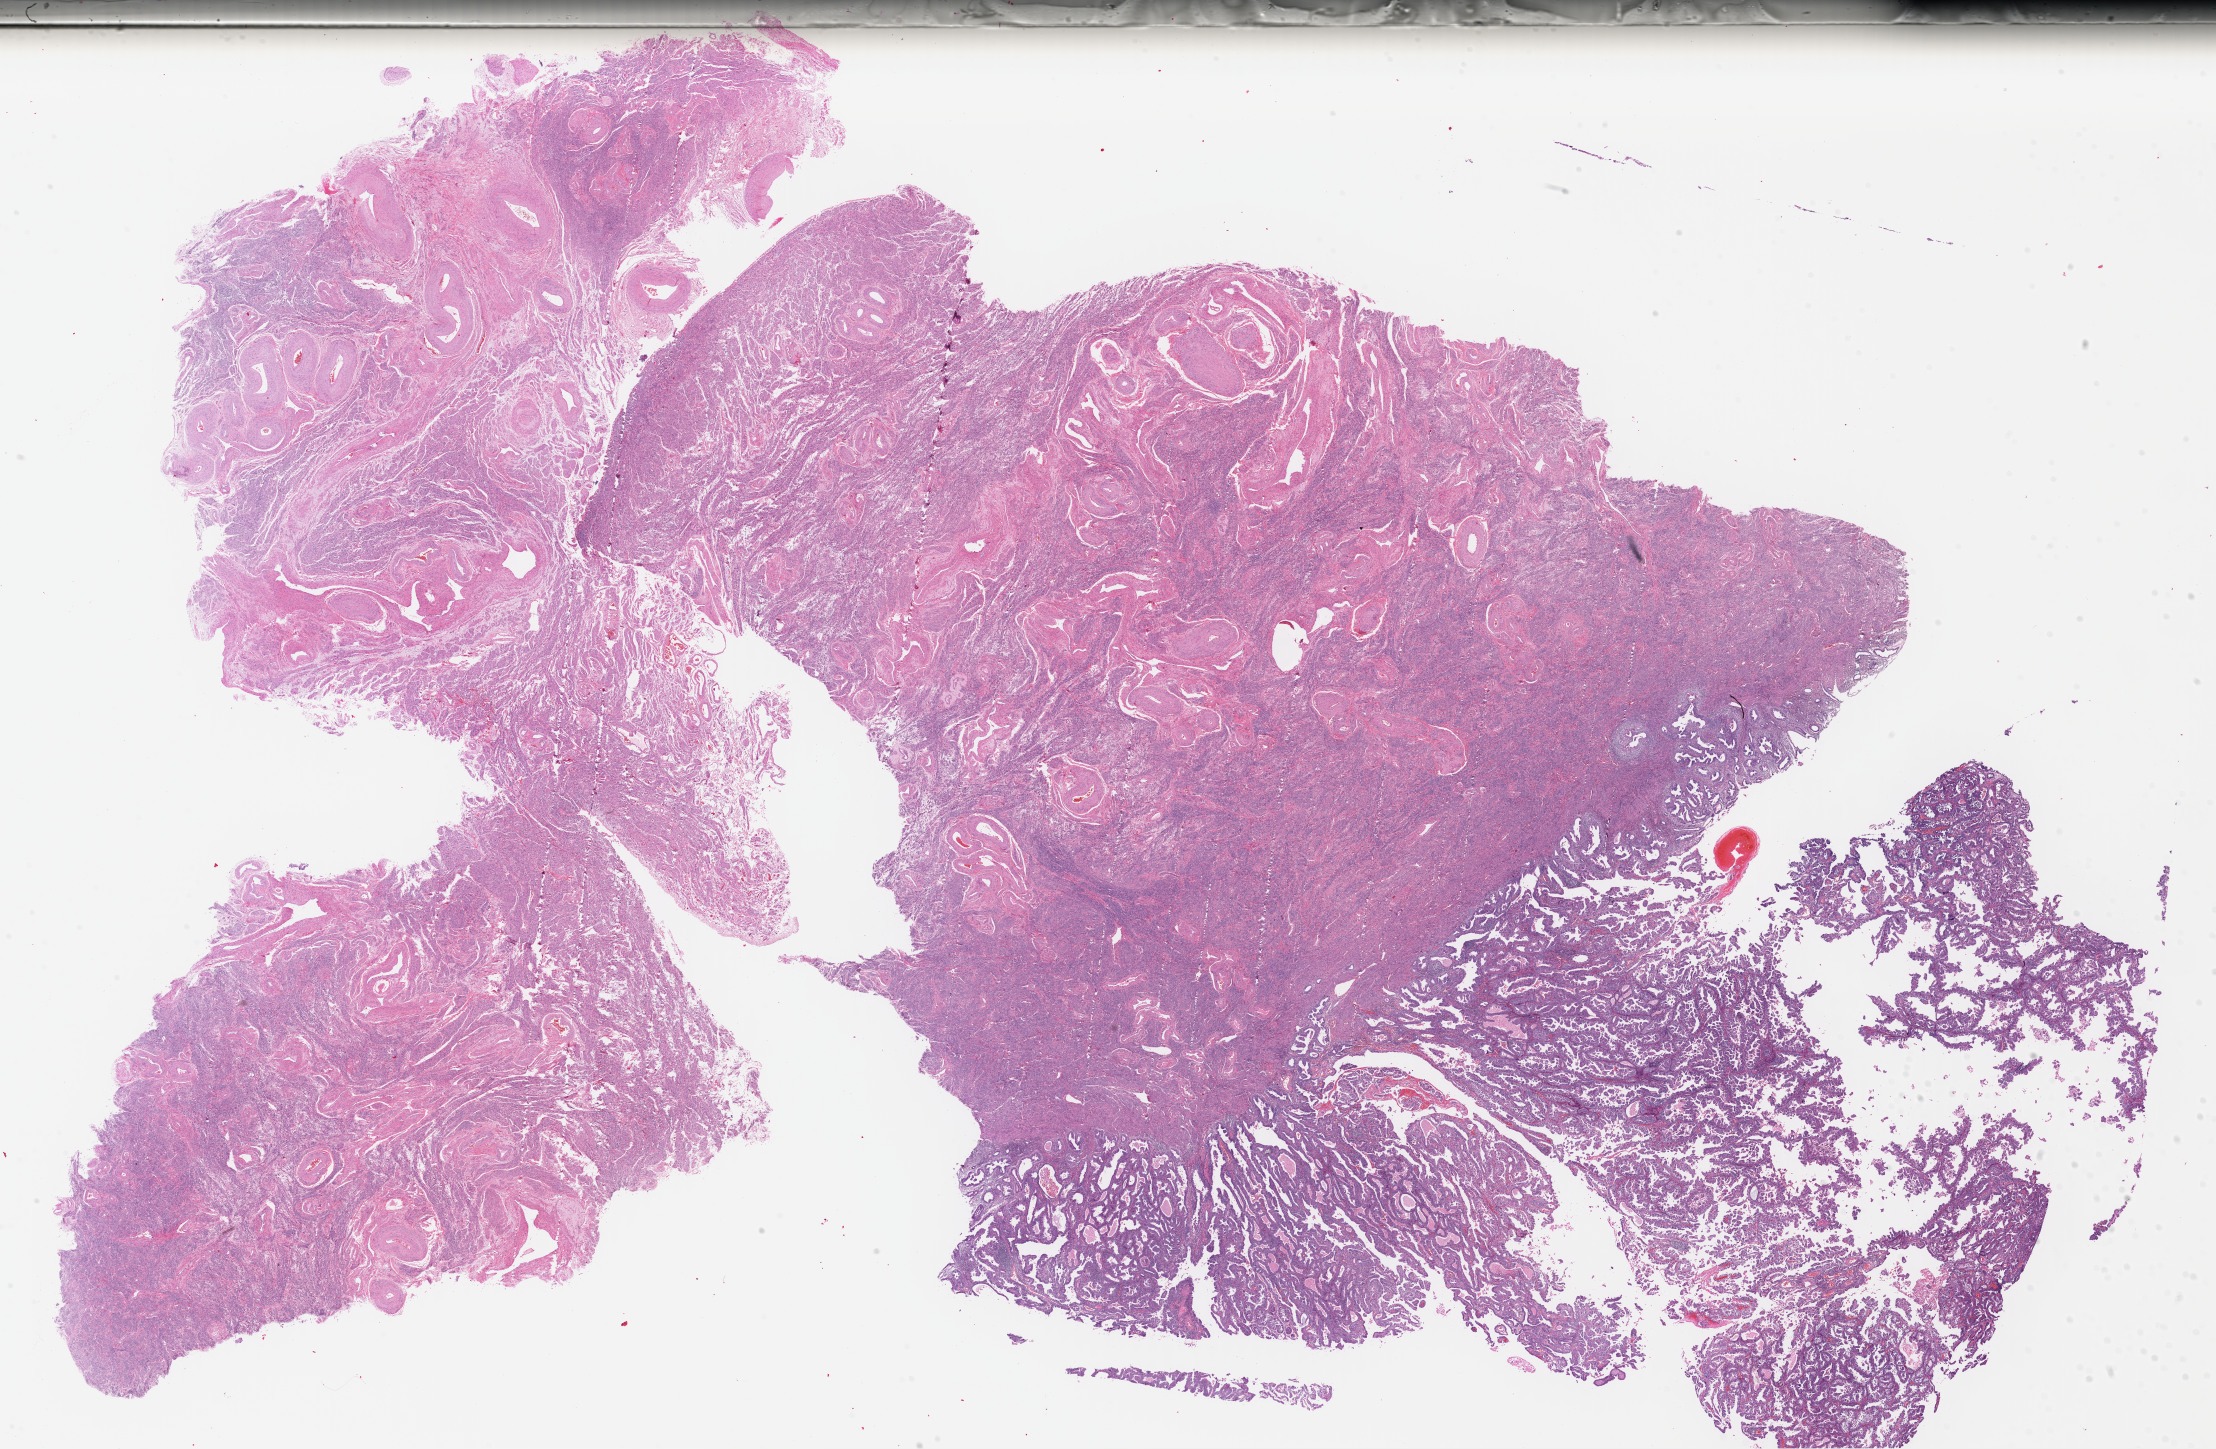
Whole-slide histology image, H&E-stained — shown as a low-resolution overview of the whole scanned area (about 34.8 x 22.8 mm, slide scanned at 40x); formalin-fixed paraffin-embedded (FFPE) diagnostic section; sample: primary tumour, uterus. Patient: female, age at initial diagnosis 71 years. Histologic grade: G3 (poorly differentiated).
Diagnosis: Serous cystadenocarcinoma, NOS (endometrium). FIGO stage: IB.